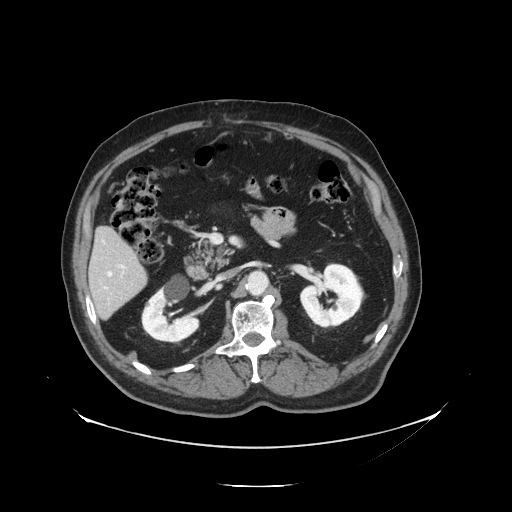
Contrast-enhanced abdominal CT, one axial slice; position 60 of 138 along the scan axis; reconstruction kernel STANDARD; intravenous contrast given; soft-tissue window (W 400 / L 40 HU); 2.5 mm slice thickness; 512 × 512 image matrix, field of view 497 × 497 mm. Male patient, age 77 years. From the clinical record (not read from this slice): diagnosis: colorectal cancer liver metastases, imaged before liver resection; multiple liver metastases: no.
Annotated regions visible in this slice (manually delineated by an expert):
- liver: bounding box <91,228,147,318> (left, top, right, bottom; pixels)
- planned liver remnant (the part of the liver to remain after resection): <91,228,142,285>
- portal vein (with intrahepatic branches): <122,266,124,269>